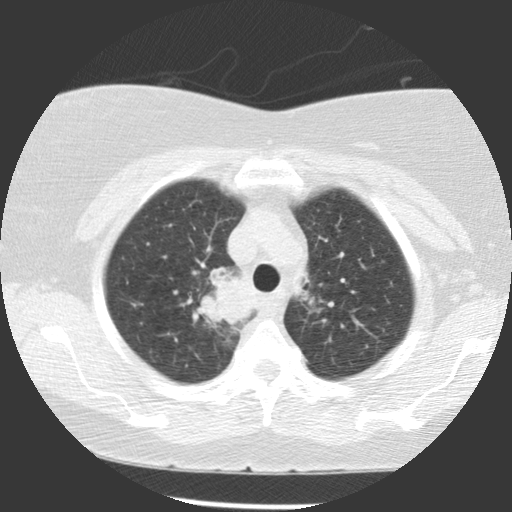
Low-dose screening chest CT, one axial slice; slice 91 of 116 in the series (ordered by position); 140 kVp; lung window (W 1500 / L -600 HU); 512 × 512 image matrix.
Outlined on this slice (expert manual segmentation):
- lesion 1 (tumor, upper lobe of right lung): bounding box [x1, y1, x2, y2] px = [196, 267, 254, 329]